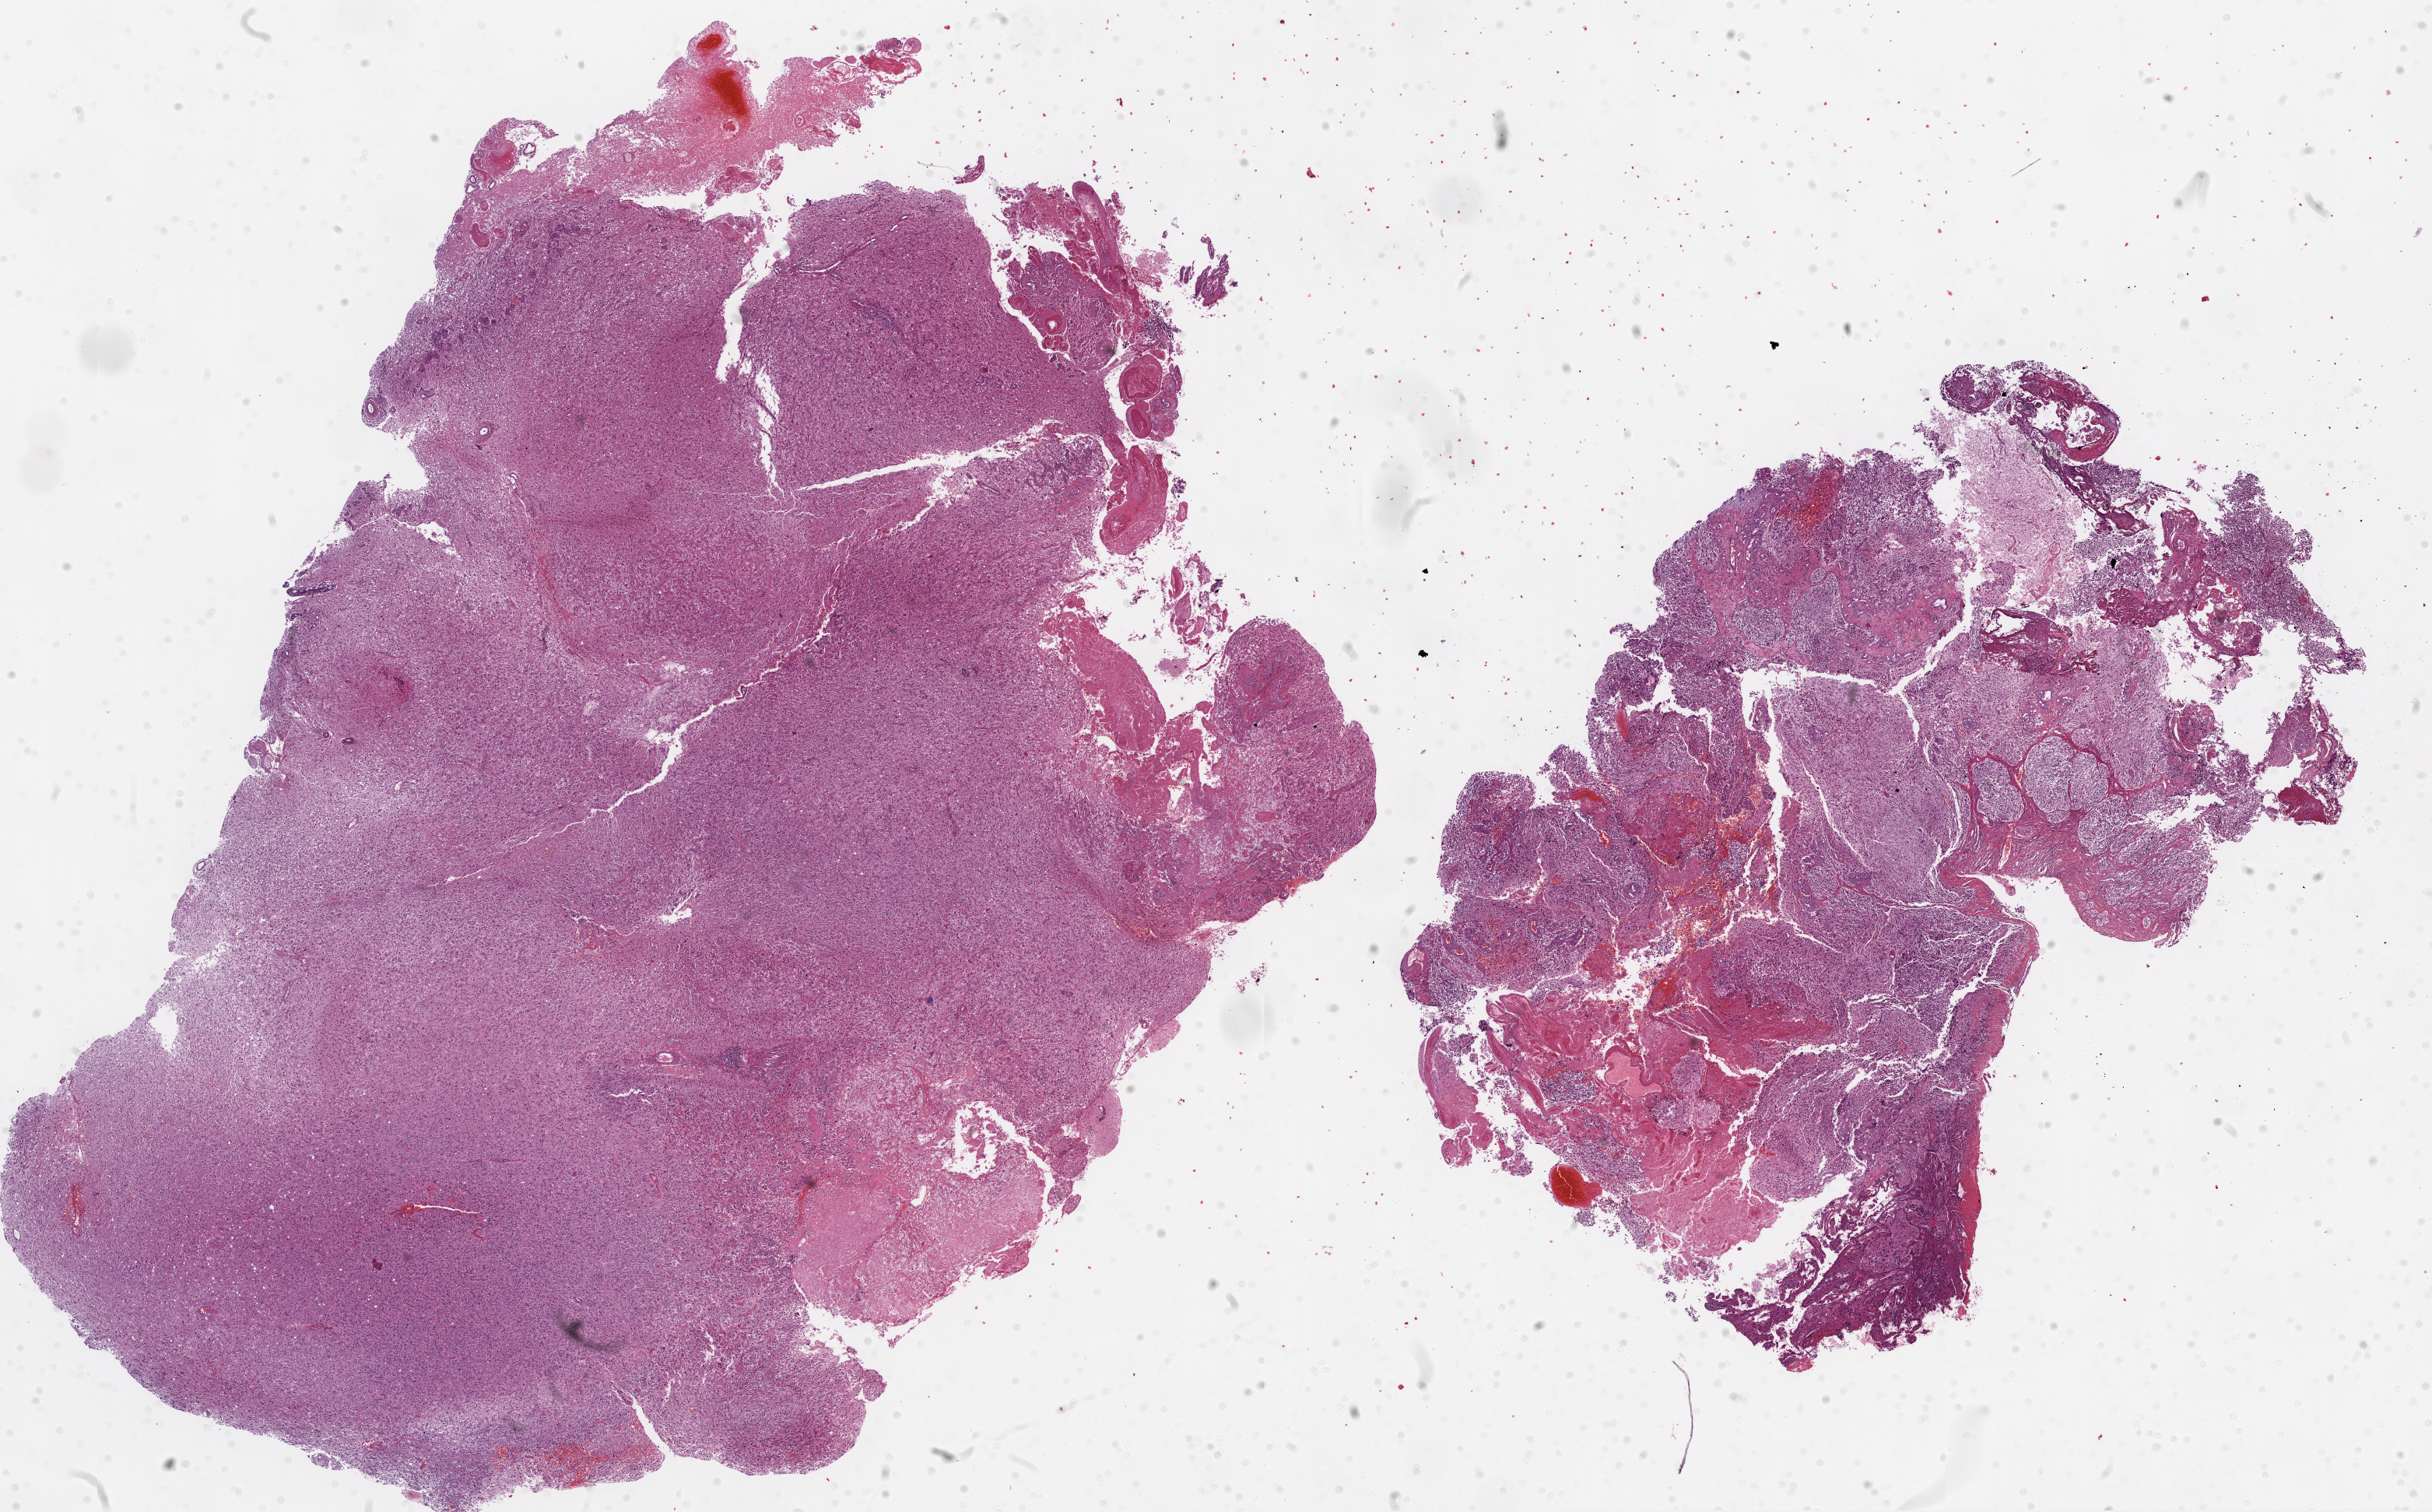
Whole-slide histology image, H&E-stained, shown as a low-resolution overview of the whole scanned area (about 25.1 x 15.6 mm, acquisition: 20x scan), formalin-fixed paraffin-embedded (FFPE) diagnostic section, primary tumour sample from the brain. Female patient; age at initial diagnosis 46 years.
Histologic diagnosis: Glioblastoma.